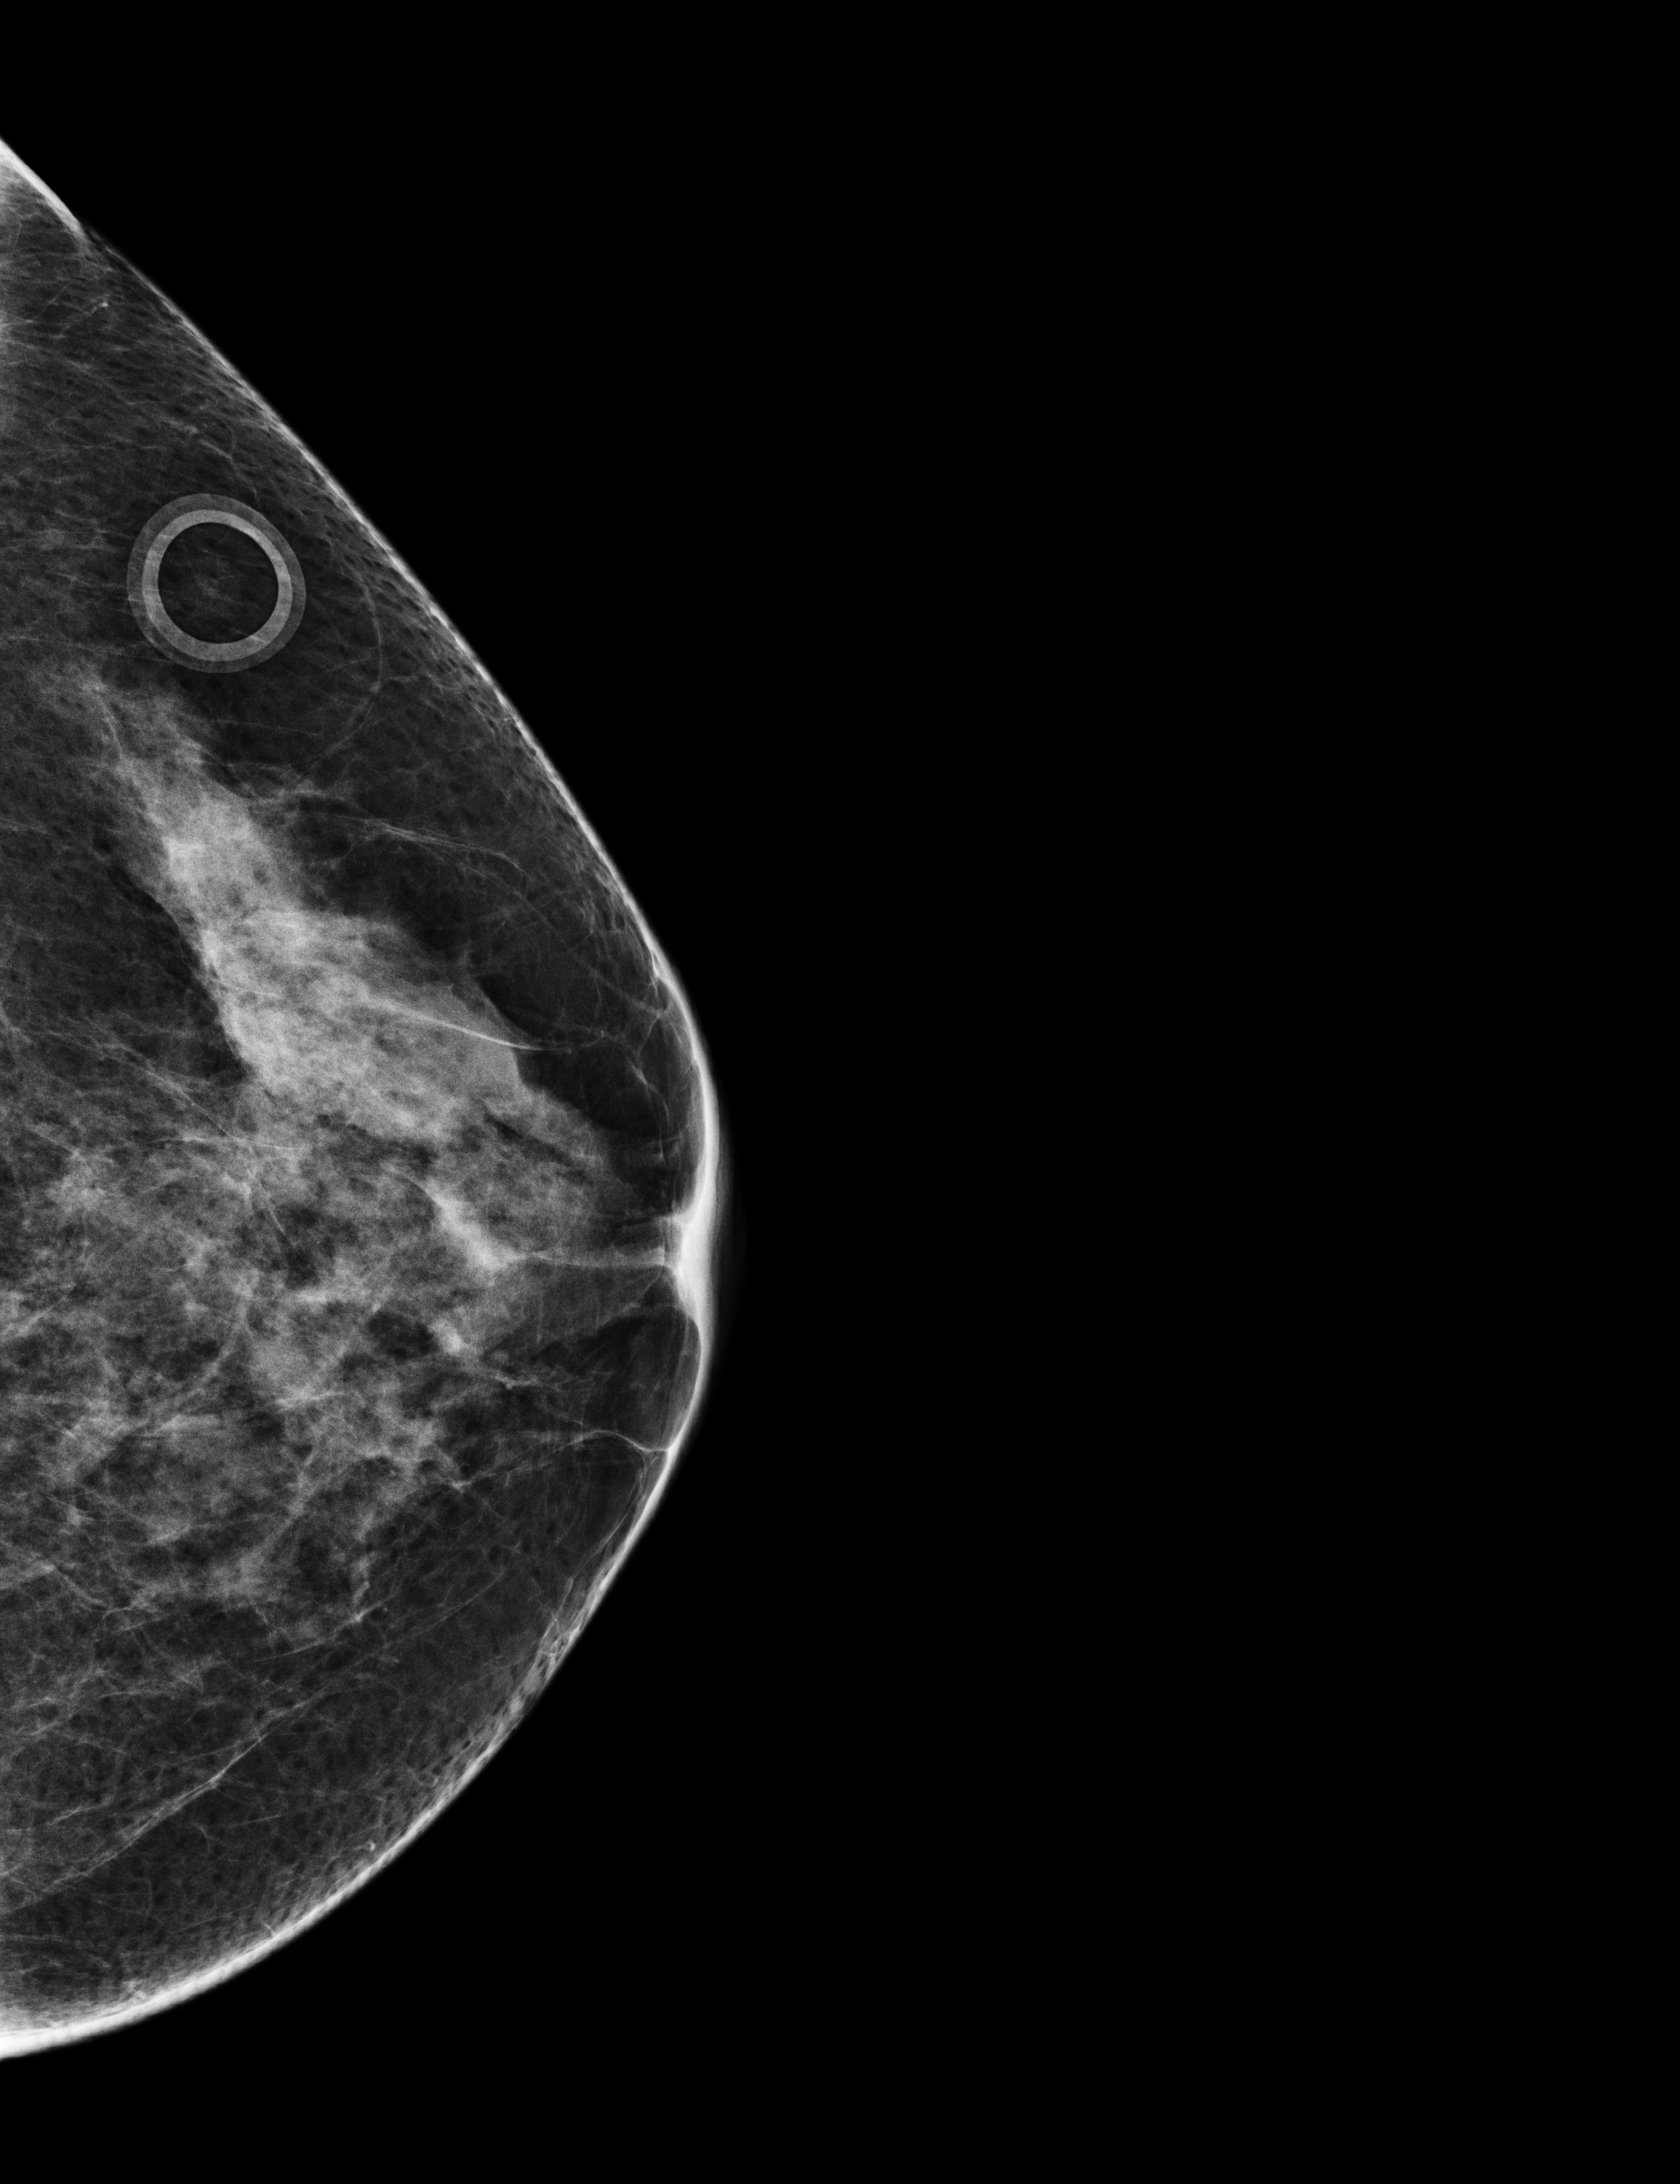
Annual screening mammography examination. Female patient, age 59 years.
Image type: full-field digital mammogram. Breast: left. Projection: cranio-caudal projection.